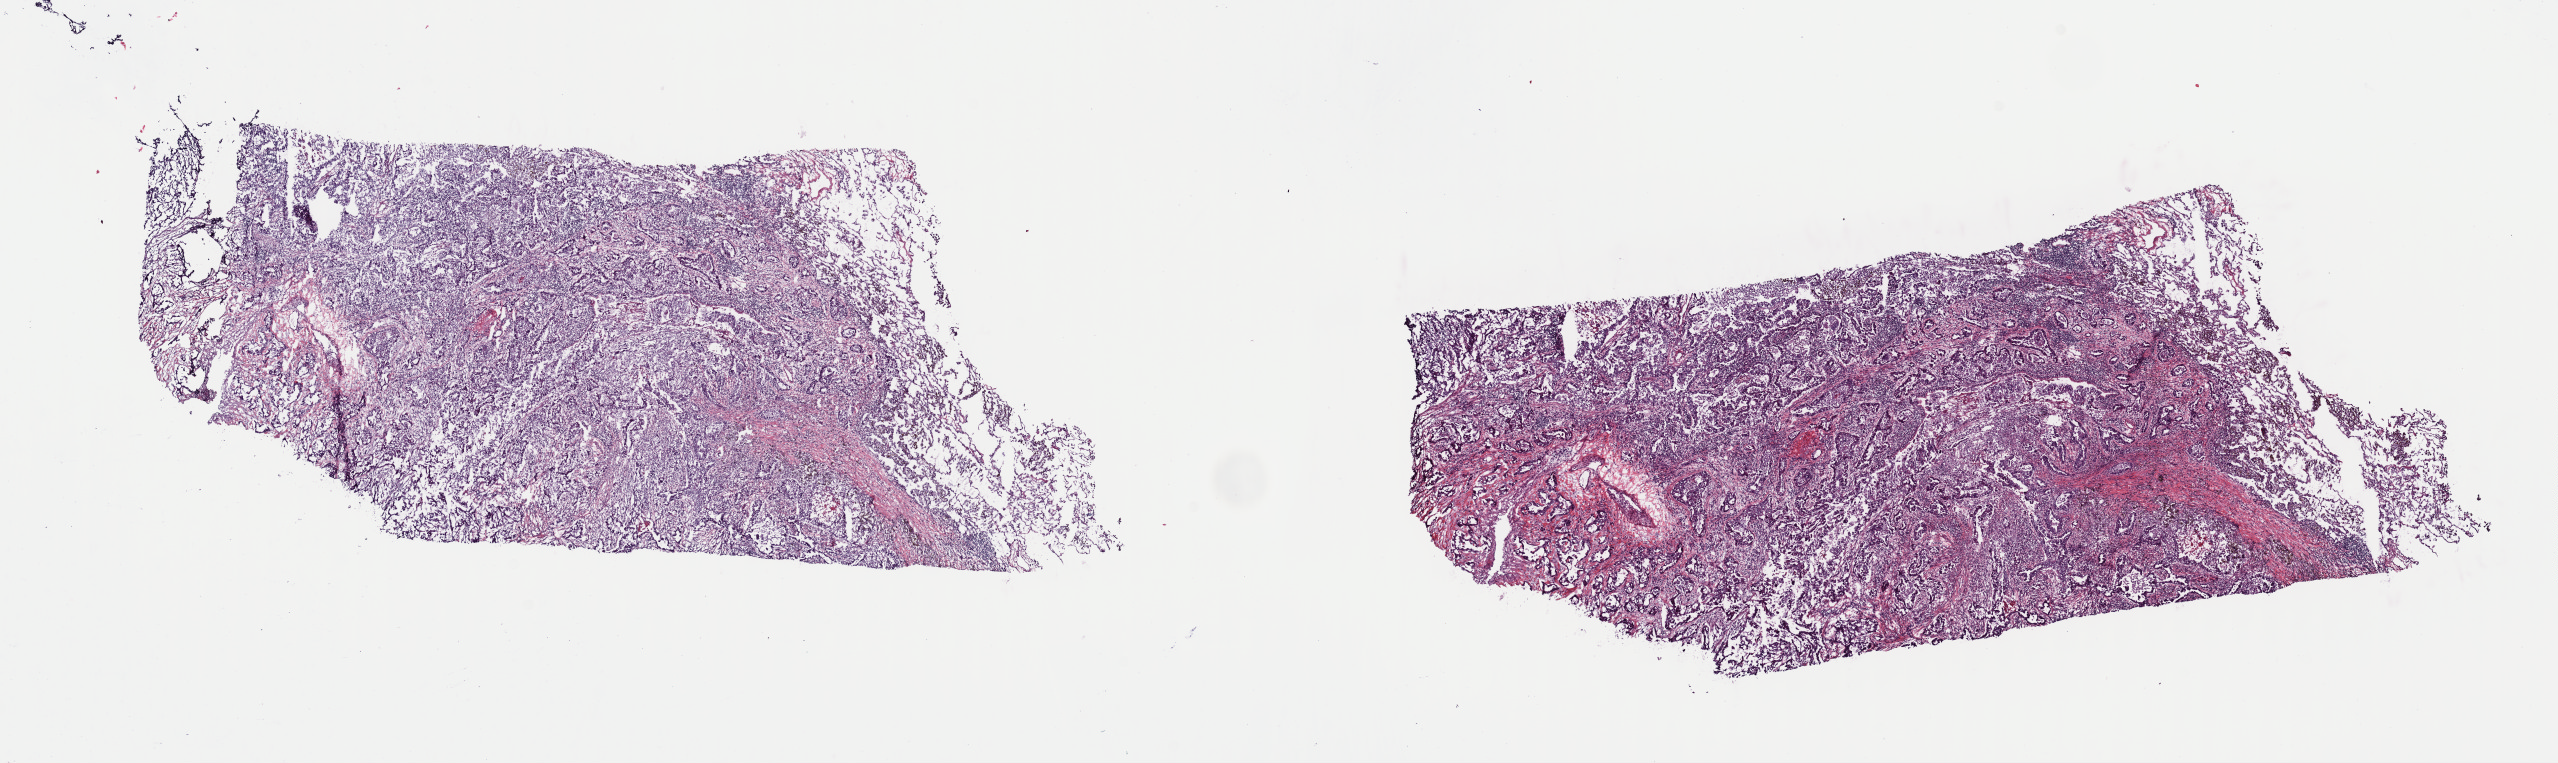
Digitized H&E tissue section (whole slide) — low-resolution overview of the scanned area, about 20.2 x 6.0 mm. Frozen section. Sample: primary tumour, lung. Male, age 53 years at initial diagnosis. Pathologist review of this section (percent, as recorded): tumour cells 60%, tumour nuclei 60%, normal cells 10%, stromal cells 30%, necrosis 0%. Infiltration values recorded for this section: lymphocyte infiltration 0%, monocyte infiltration 0%, neutrophil infiltration 0%.
Histologic diagnosis: Adenocarcinoma, NOS (upper lobe, lung). AJCC pathologic stage: IIB (5th edition).